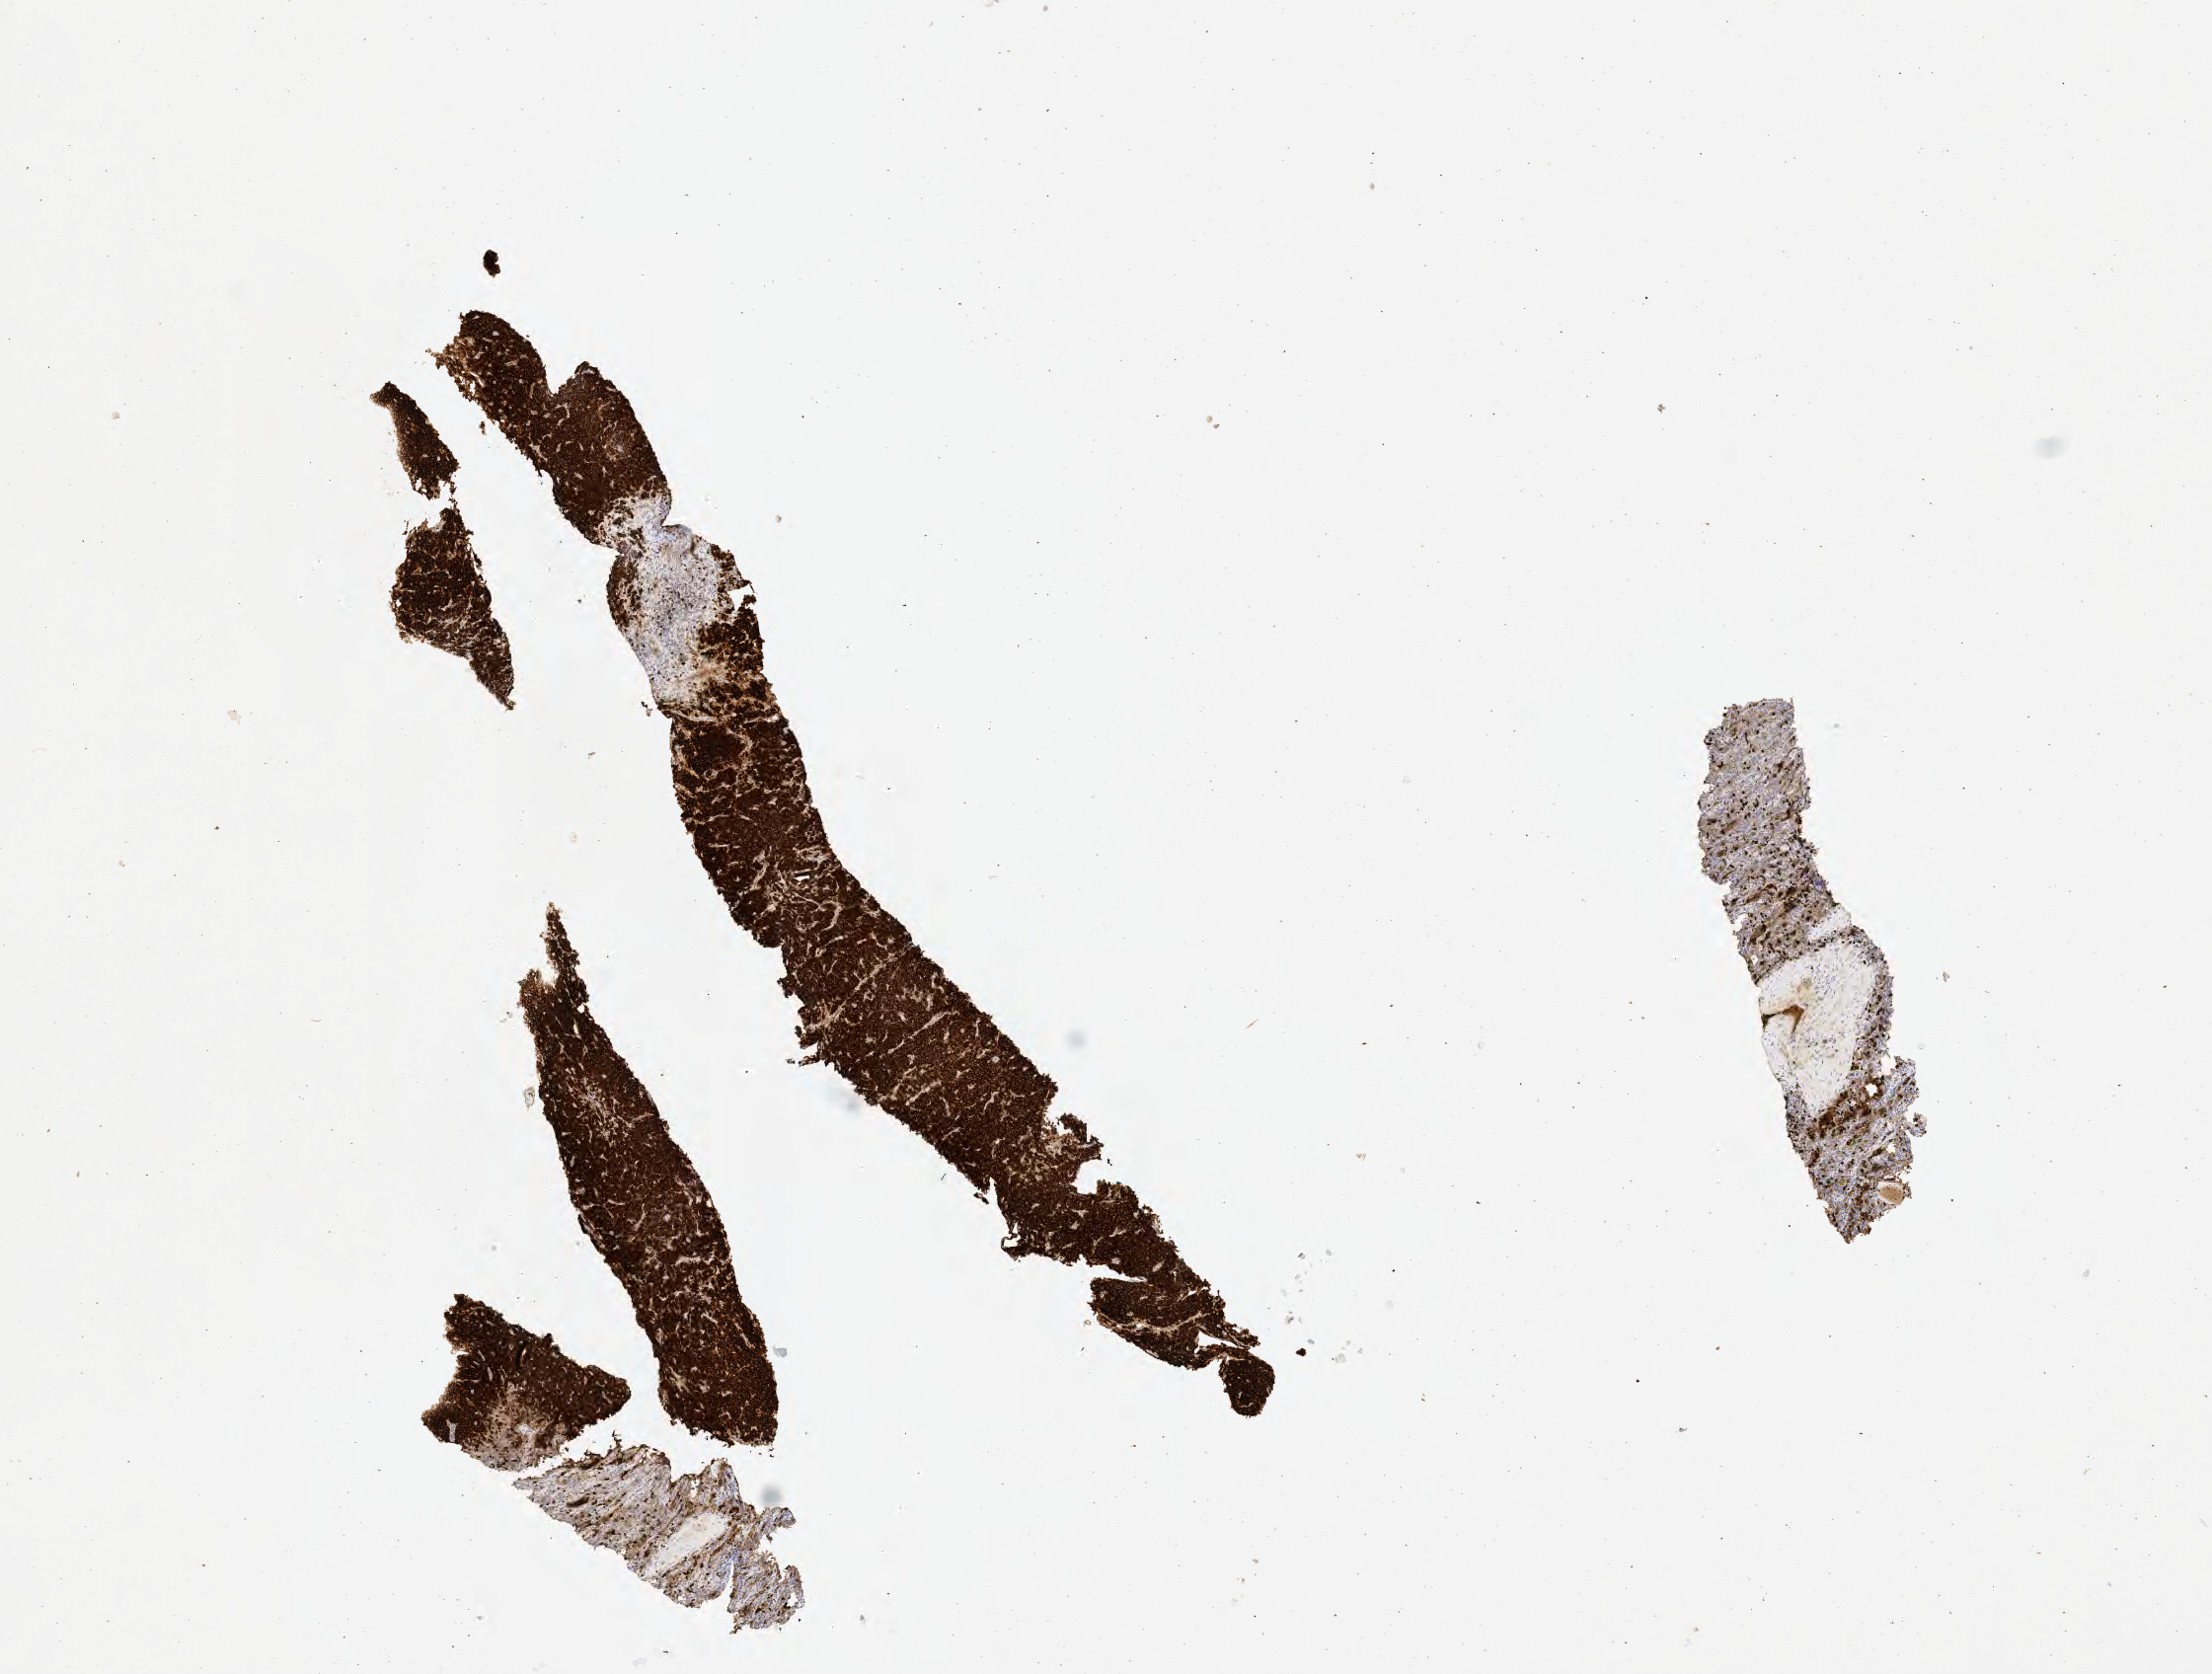
Whole-slide image, immunohistochemical stain for CD20 — a low-resolution overview of the entire scanned area, about 9.1 x 6.9 mm. Tumor tissue. Patient: male, 13 years old.
Histologic diagnosis: Diffuse large B-cell lymphoma, NOS.